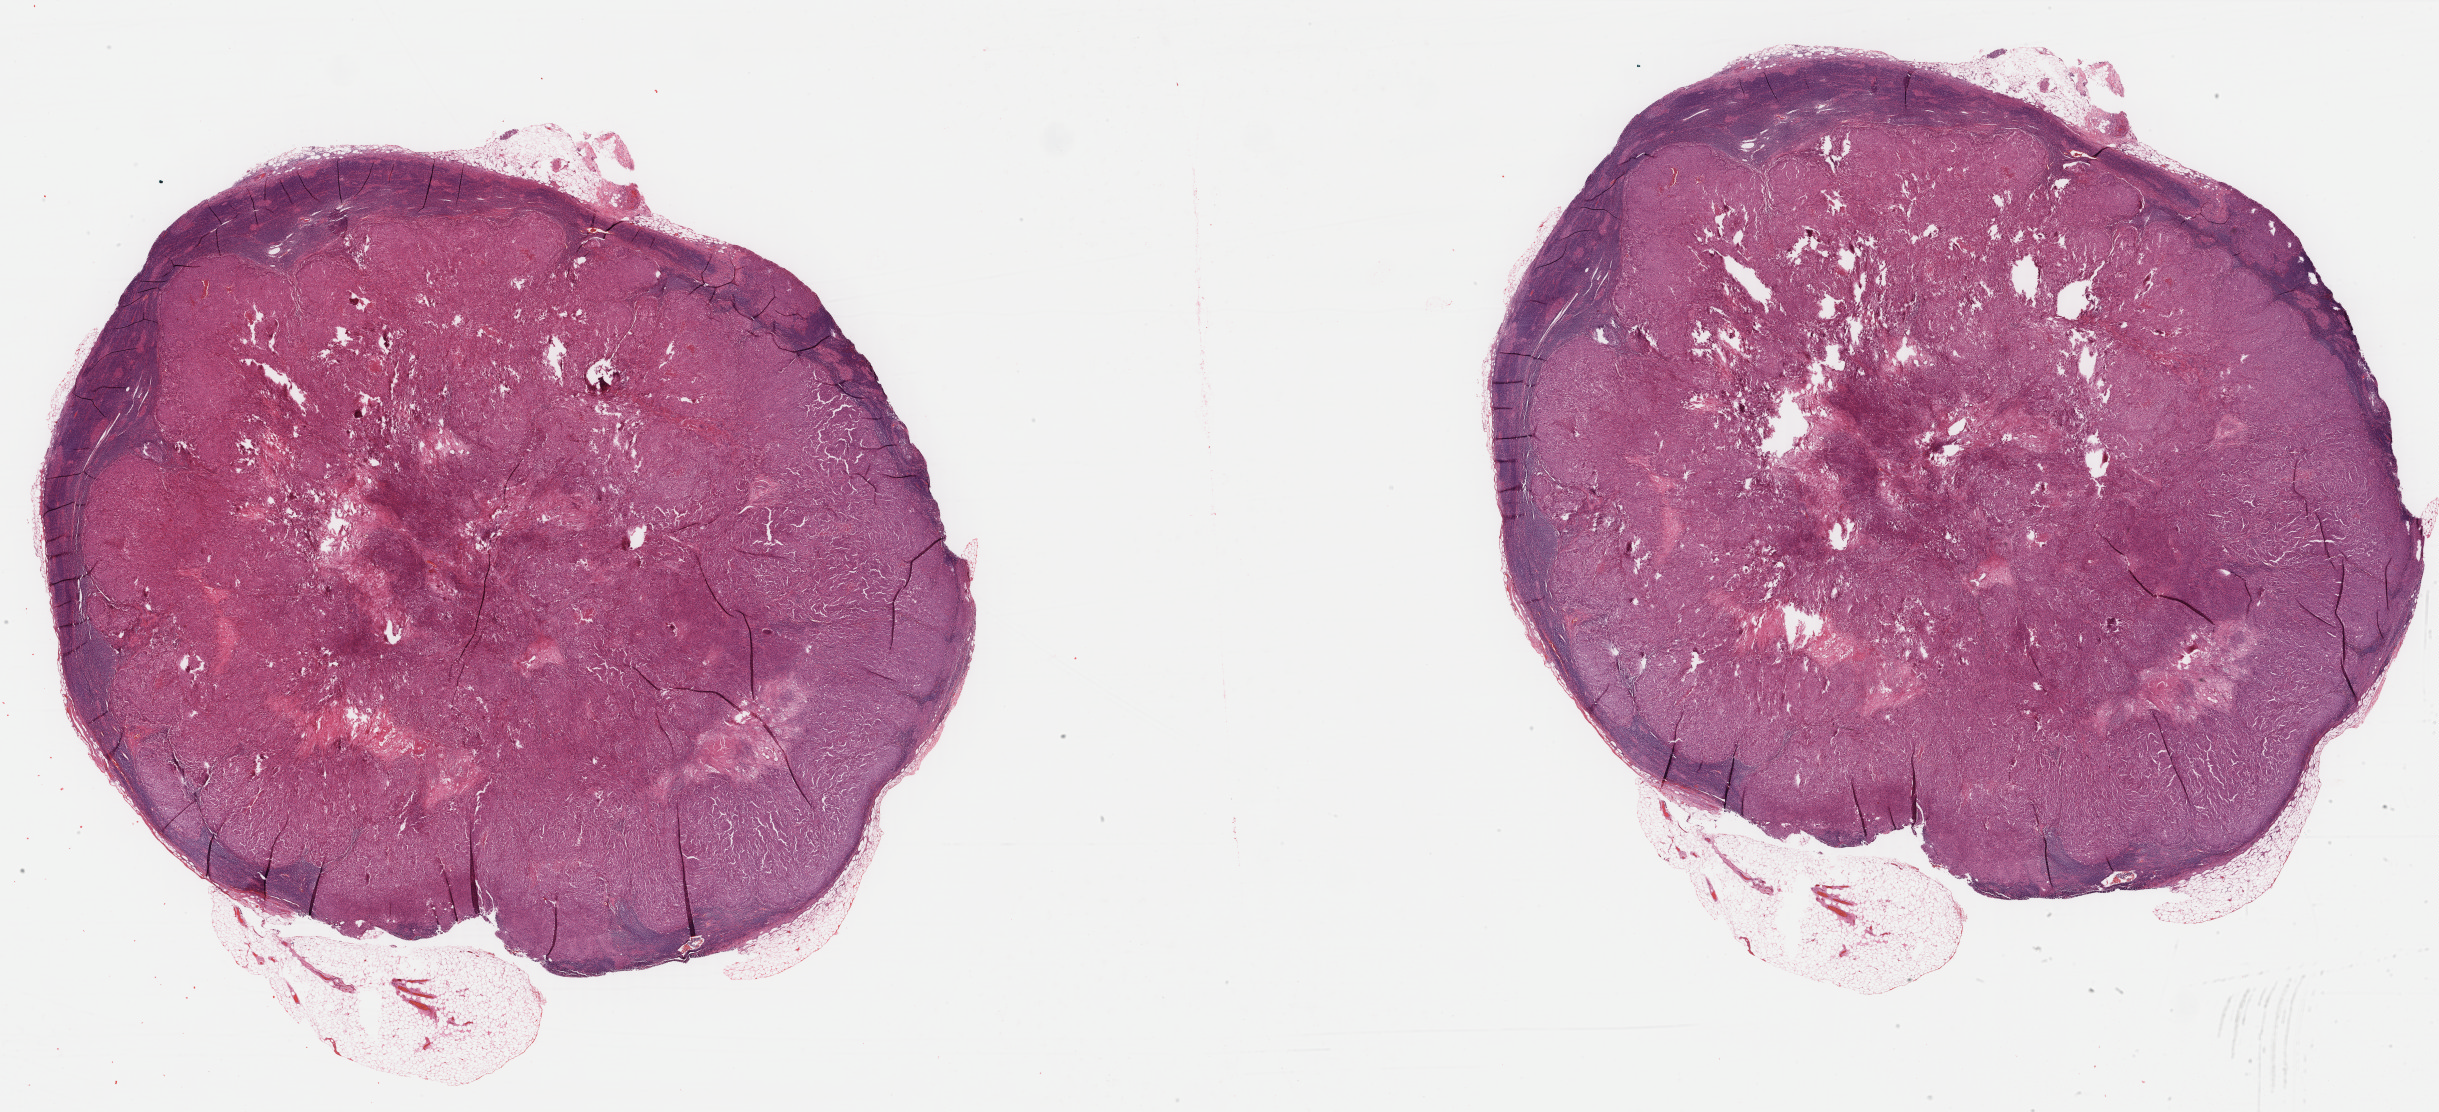
Hematoxylin and eosin (H&E) stained whole-slide image, a low-resolution overview of the entire scanned area, about 38.7 x 17.7 mm (slide scanned at 40x), formalin-fixed paraffin-embedded (FFPE) diagnostic section, sample: primary tumour, skin. Male, age 77 years at initial diagnosis.
* histologic diagnosis: Malignant melanoma, NOS